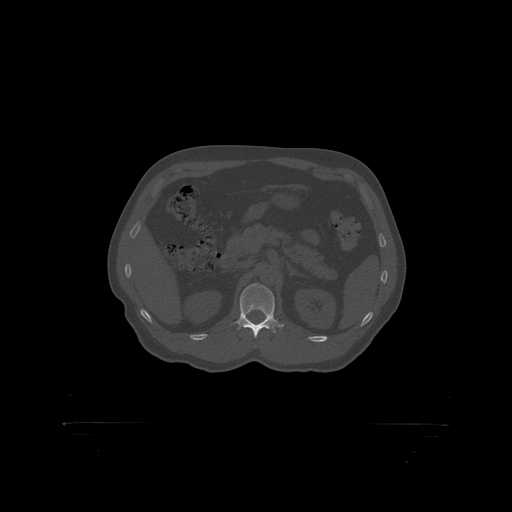
CT including the spine, one axial slice. Position 326 of 399 along the scan axis. 120 kVp. Bone window (W 1800 / L 400 HU). 1.25 mm slice thickness. 512 × 512 image matrix, field of view 650 × 650 mm. Male patient, age 46 years. Case-level facts recorded for this patient, not image findings: primary cancer: skin.
Outlined on this slice (semi-automatic segmentation, software-assisted and operator-edited):
- L1 vertebra: bounding box [x1, y1, x2, y2] px = [240, 284, 276, 319]